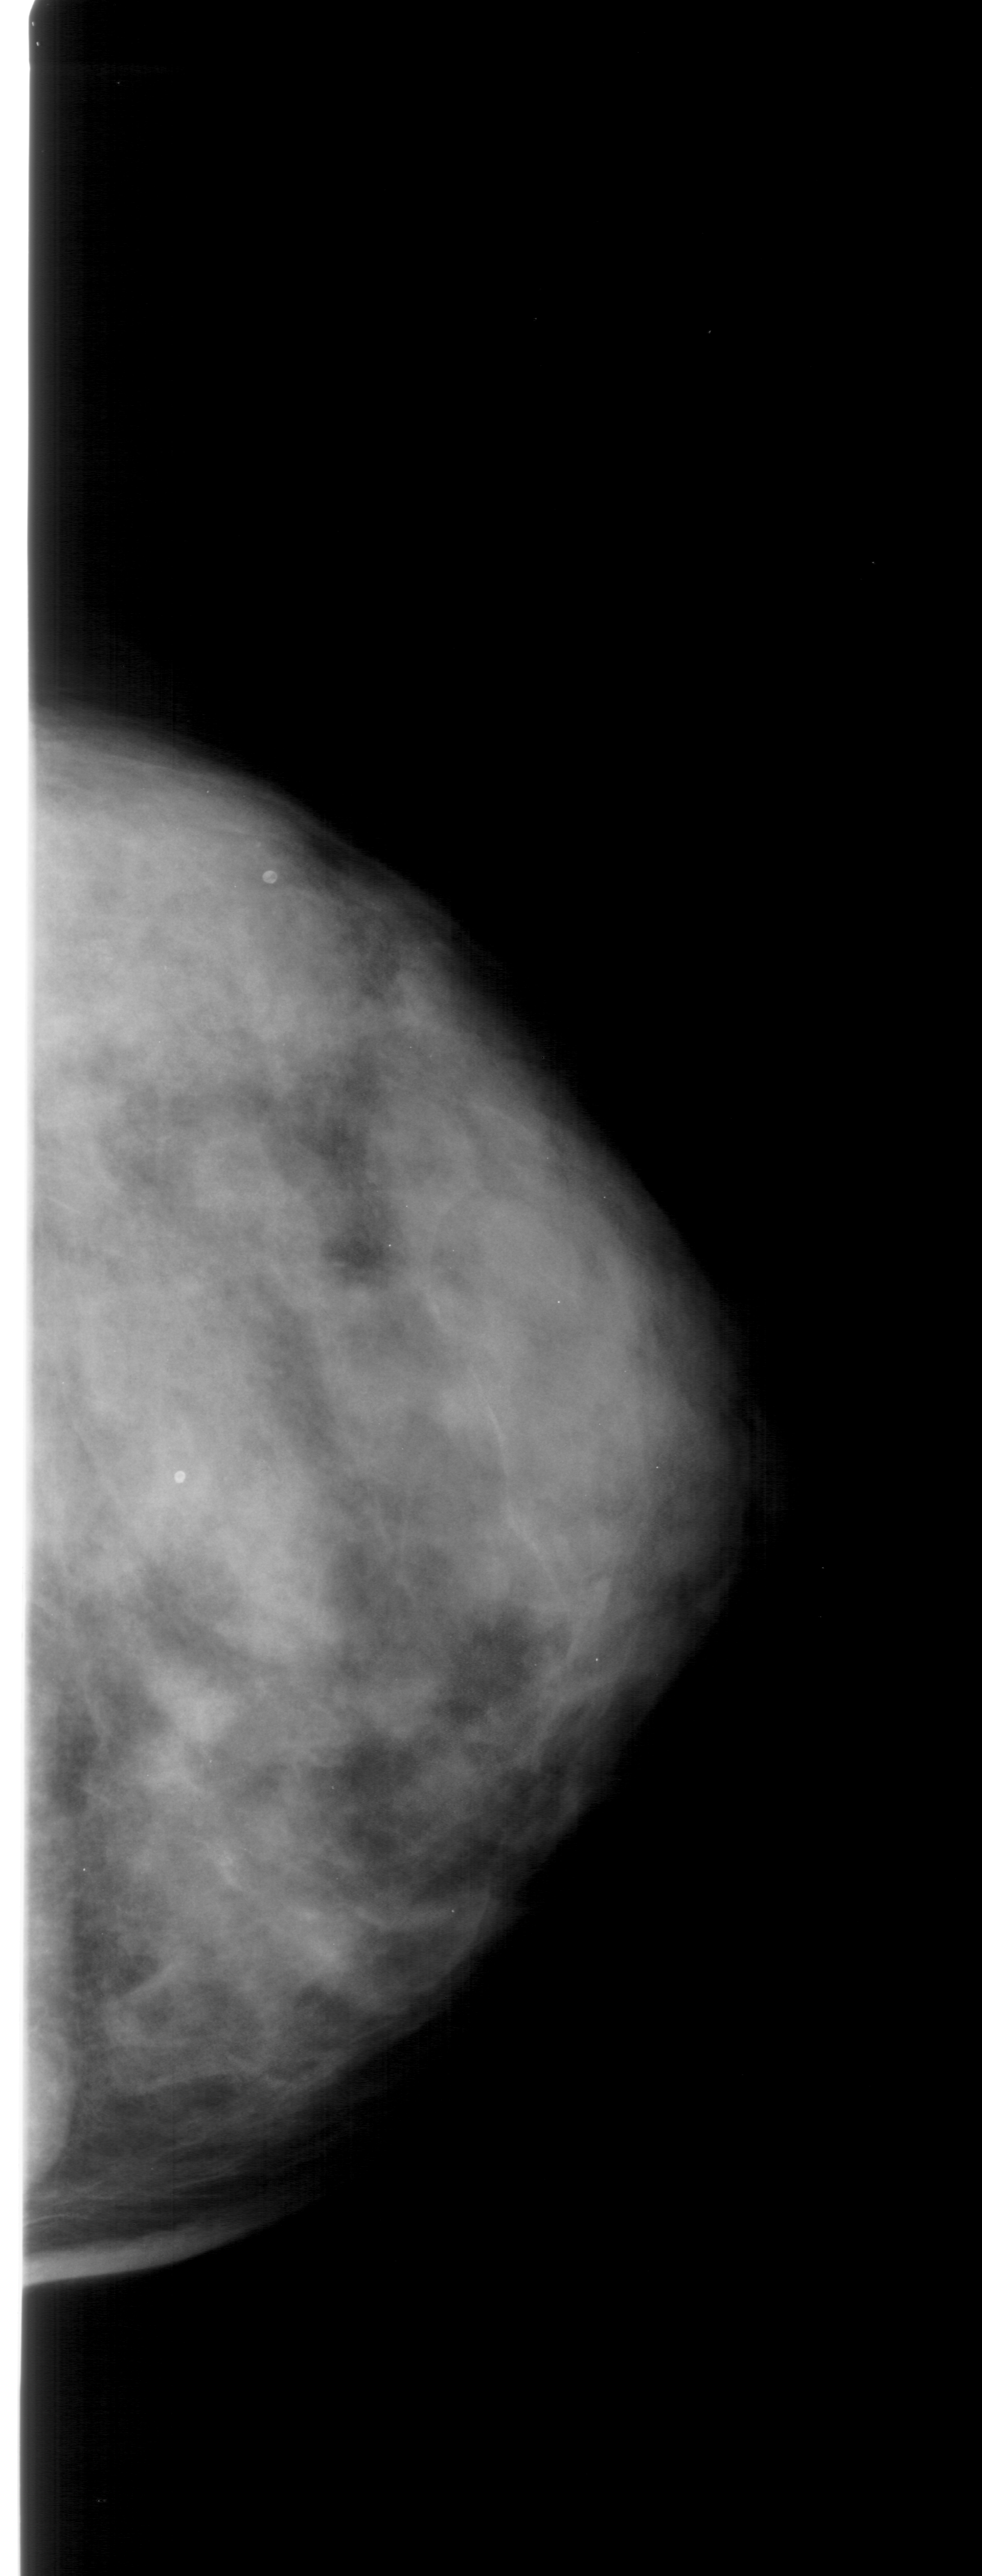
Scanned film-screen mammogram; right breast; CC view; breast composition: extremely dense (BI-RADS density category 4 of 4); 982 × 2576 image matrix.
Expert-marked regions of interest on this film, with their recorded descriptors:
- calcifications, morphology punctate, distribution segmental; BI-RADS assessment category 4; subtlety rating 1 on a 1 (subtle) to 5 (obvious) scale; pathology (as recorded): benign: bounding box <63,796,375,1071> (left, top, right, bottom; pixels)